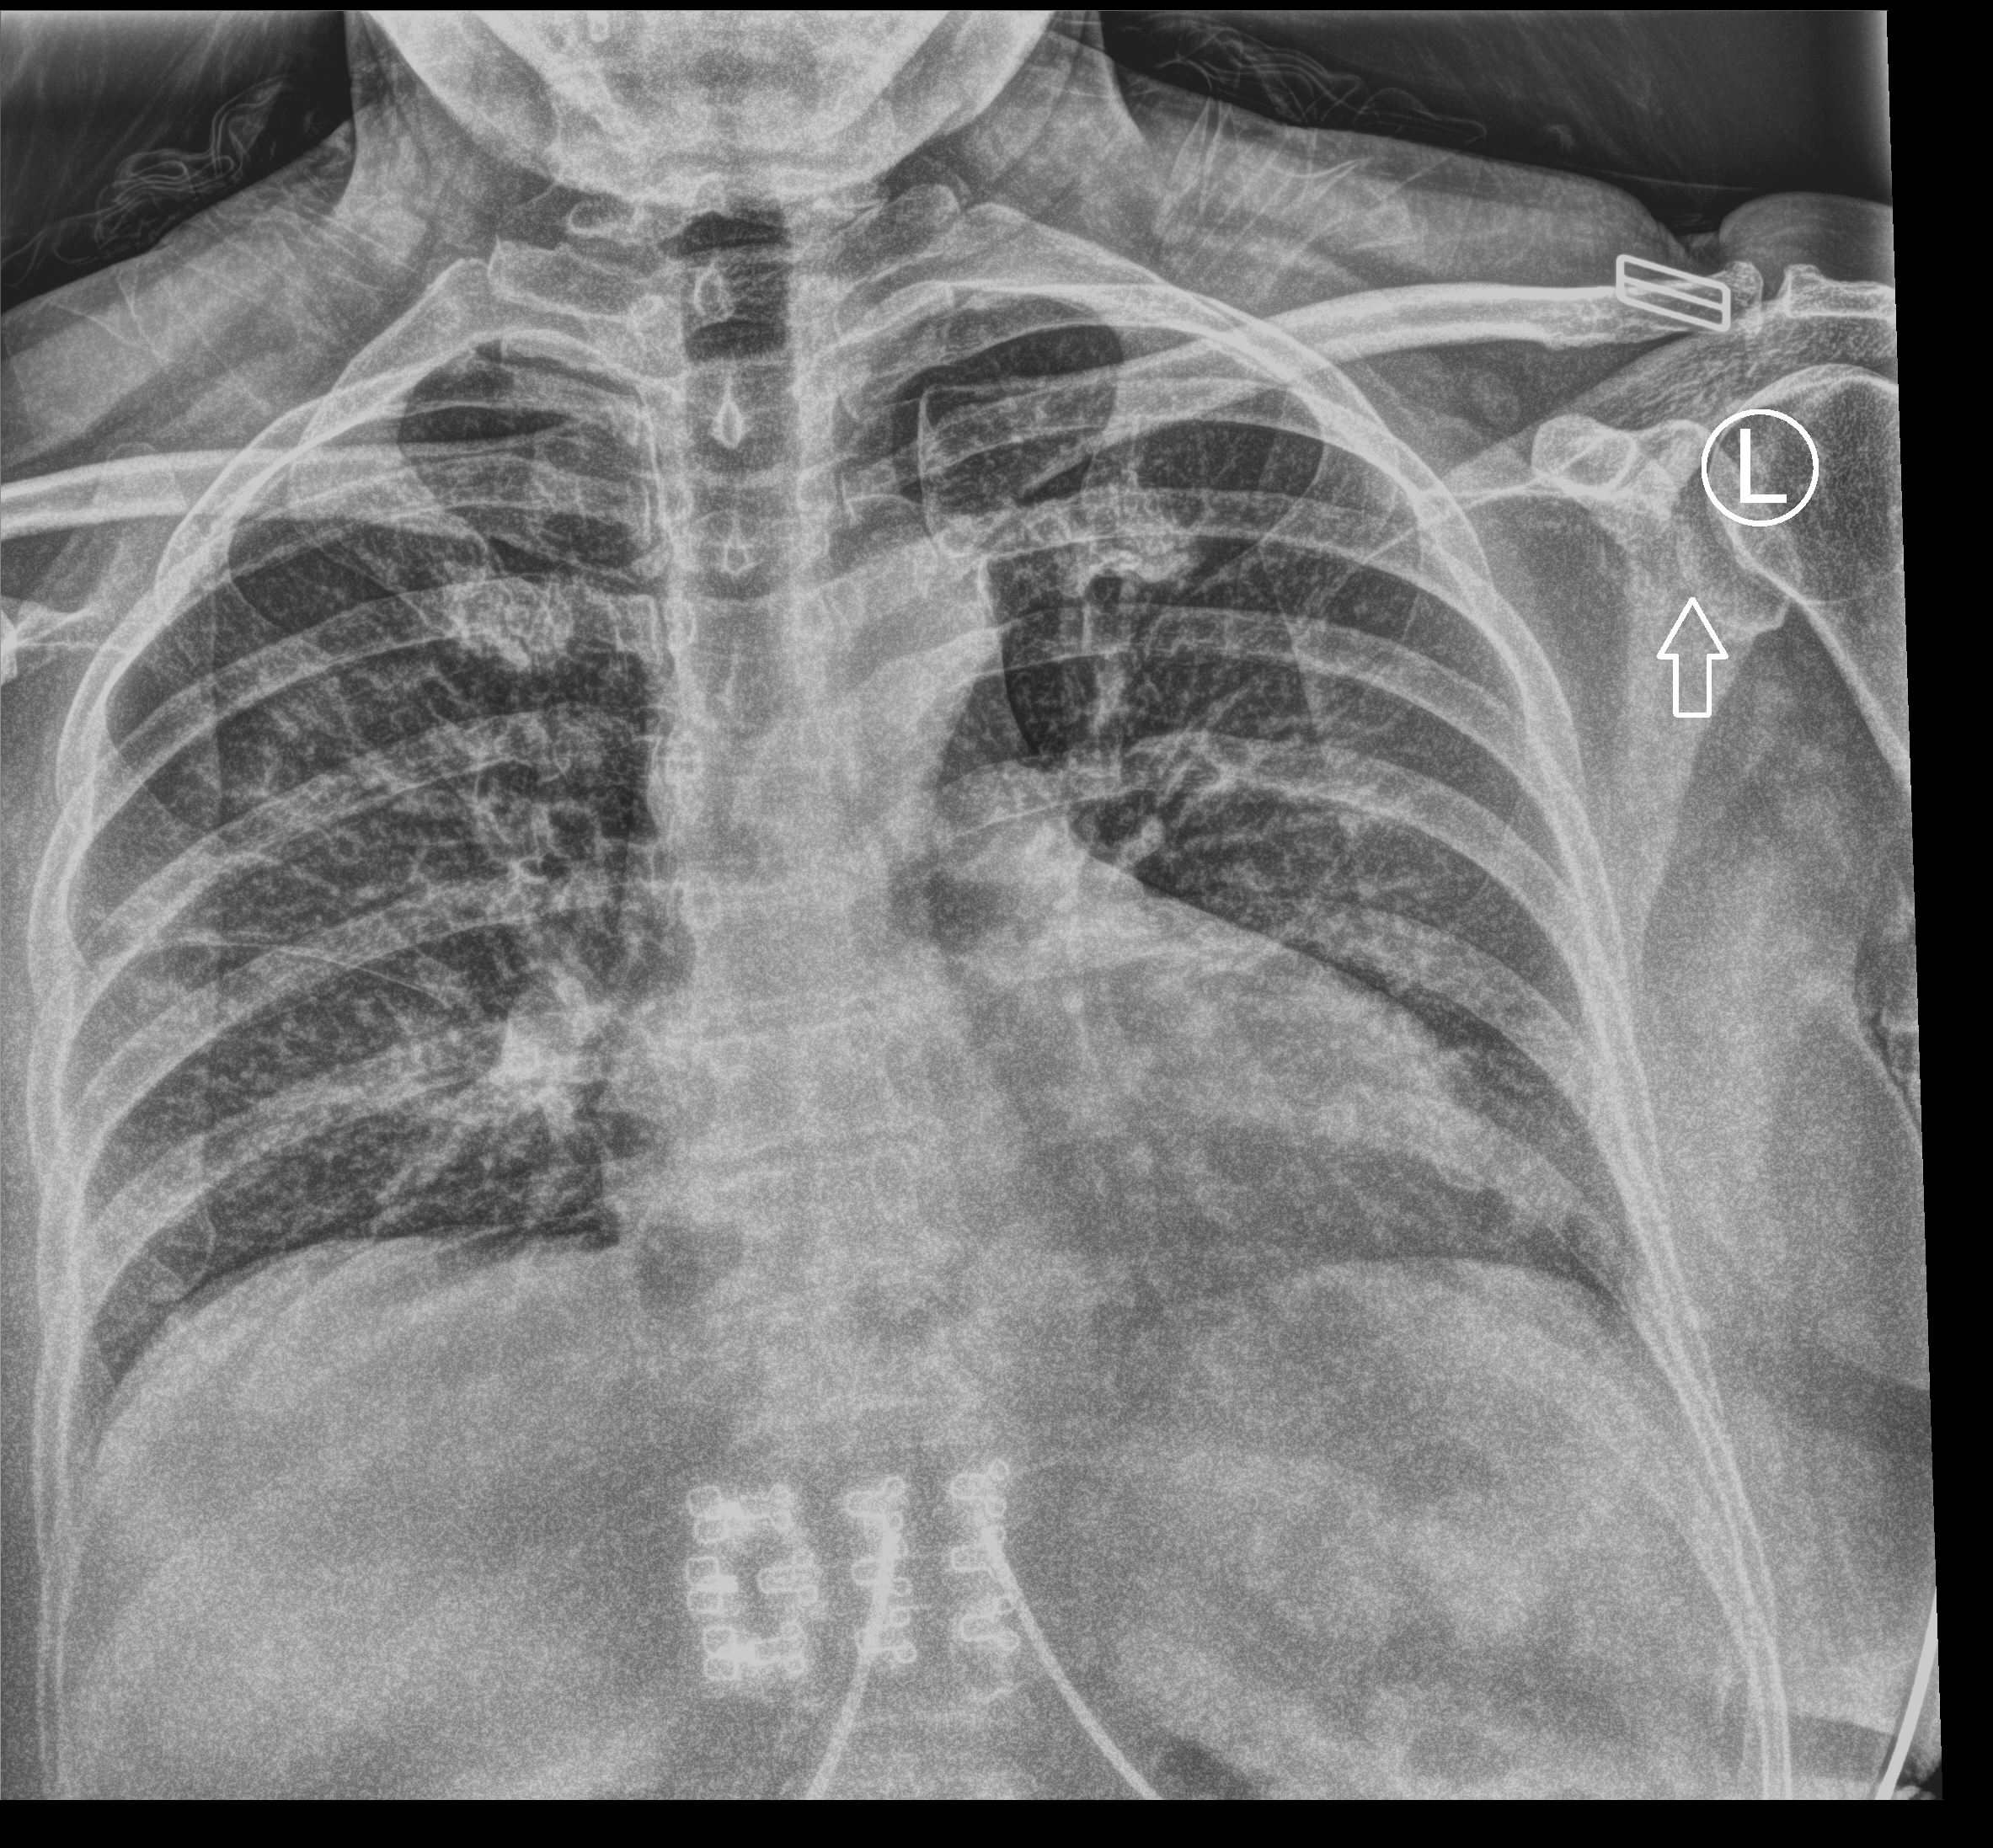
Chest X-ray (portable), anteroposterior (AP) projection. Patient hospitalised with COVID-19; female, aged 60–74 years.
From the hospital-stay record, not from the radiograph (when in the stay this image was taken is not recorded): mechanically ventilated during this hospital stay: no; admitted to intensive care during this hospital stay: no.